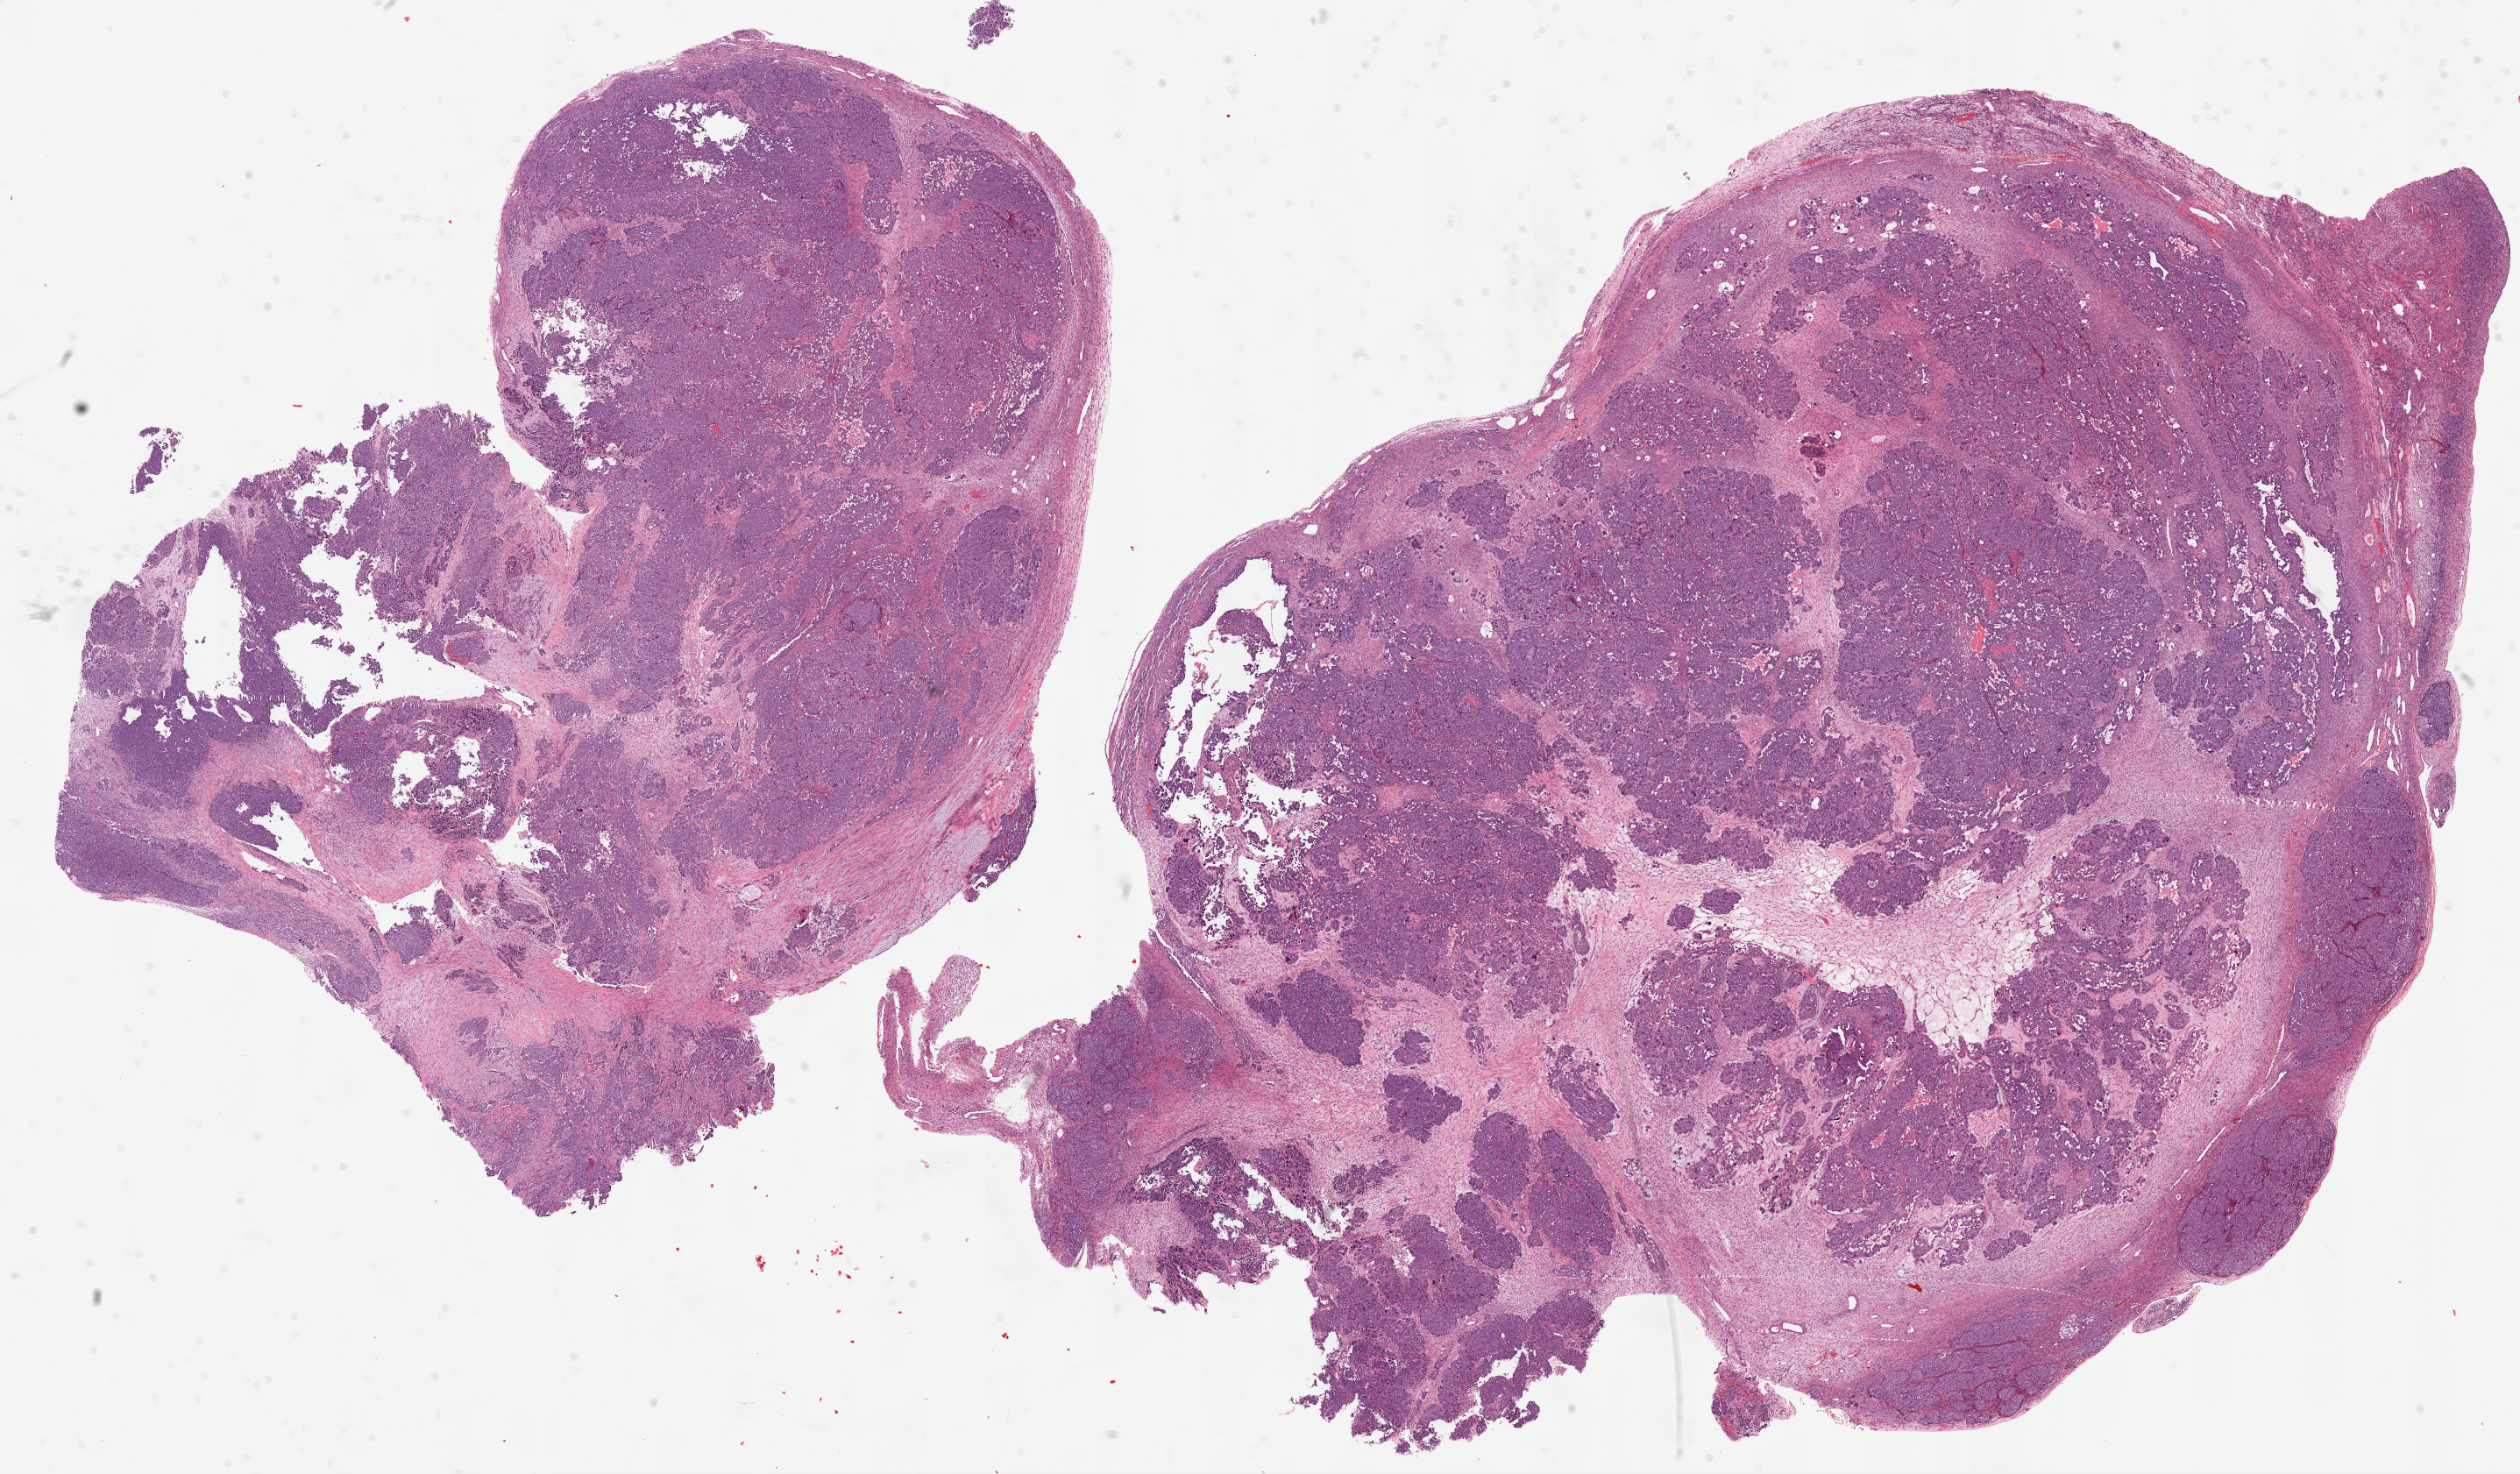
Whole-slide histology image, H&E-stained, low-resolution overview of the scanned area, about 23.1 x 13.5 mm (acquisition: 20x scan). Frozen section from the top of the tissue portion. Primary tumour sample from the ovary. Female, age 37 years at initial diagnosis. Histologic grade: G3 (poorly differentiated). Slide review estimates, as recorded: tumour cells 68%, tumour nuclei 75%, normal cells 0%, stromal cells 20%, necrosis 12%.
Pathologic diagnosis: Serous cystadenocarcinoma, NOS. Laterality: right. FIGO stage: IIIB.